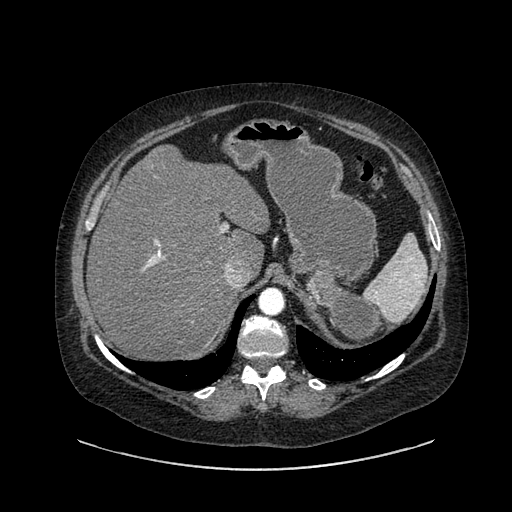
Contrast-enhanced abdominal CT, one axial slice; slice 630 of 769 in the series (ordered by position); reconstruction kernel SOFT; 120 kVp; intravenous contrast given; soft-tissue window (W 400 / L 40 HU); 0.62 mm slice thickness; 512 × 512 image matrix, field of view 460 × 460 mm. Female patient, age 61 years. From the clinical record (not read from this slice): diagnosis: adrenocortical carcinoma; tumour side: left adrenal; tumour size at pathology: 13 cm; Ki-67 index: 79 %; stage (as recorded): 2.
Structures marked on this image (semi-automatic segmentation, software-assisted and operator-edited):
- mass: bounding box <305,271,378,344> (left, top, right, bottom; pixels)